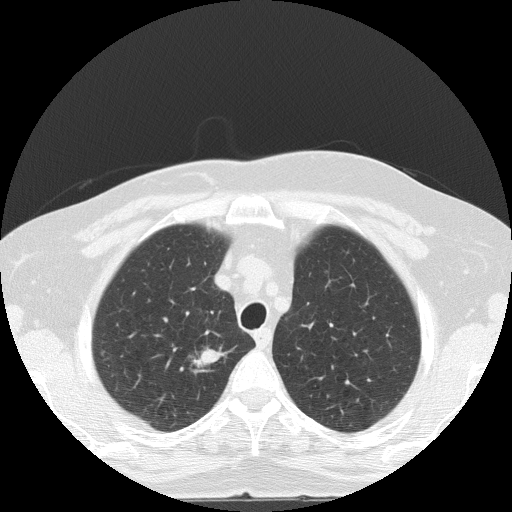
Low-dose screening chest CT, one axial slice; position 109 of 133 along the scan axis; reconstruction kernel FC51; 120 kVp; lung window (W 1500 / L -600 HU); 512 × 512 image matrix, field of view 320 × 320 mm.
Annotated regions visible in this slice (outlined manually by an expert reader):
- lesion 1 (tumor, upper lobe of right lung): bounding box (x1, y1, x2, y2) in pixels: (193, 348, 225, 371)